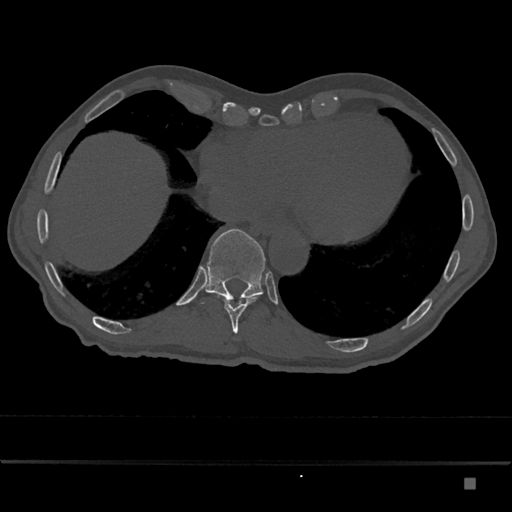
CT including the spine, one axial slice; slice 711 of 797 in the series (ordered by position); reconstruction kernel Br40s/3; bone window (W 1800 / L 400 HU); 0.5 mm slice thickness; 512 × 512 image matrix, field of view 390 × 390 mm. Patient: male, 72 years. From the clinical record (not read from this slice): primary cancer: prostate.
Annotated regions visible in this slice (semi-automatically segmented with operator editing):
- T10 vertebra: box from (x=224, y=297) to (x=256, y=334) px
- T11 vertebra: (x=200, y=229)–(x=265, y=304)